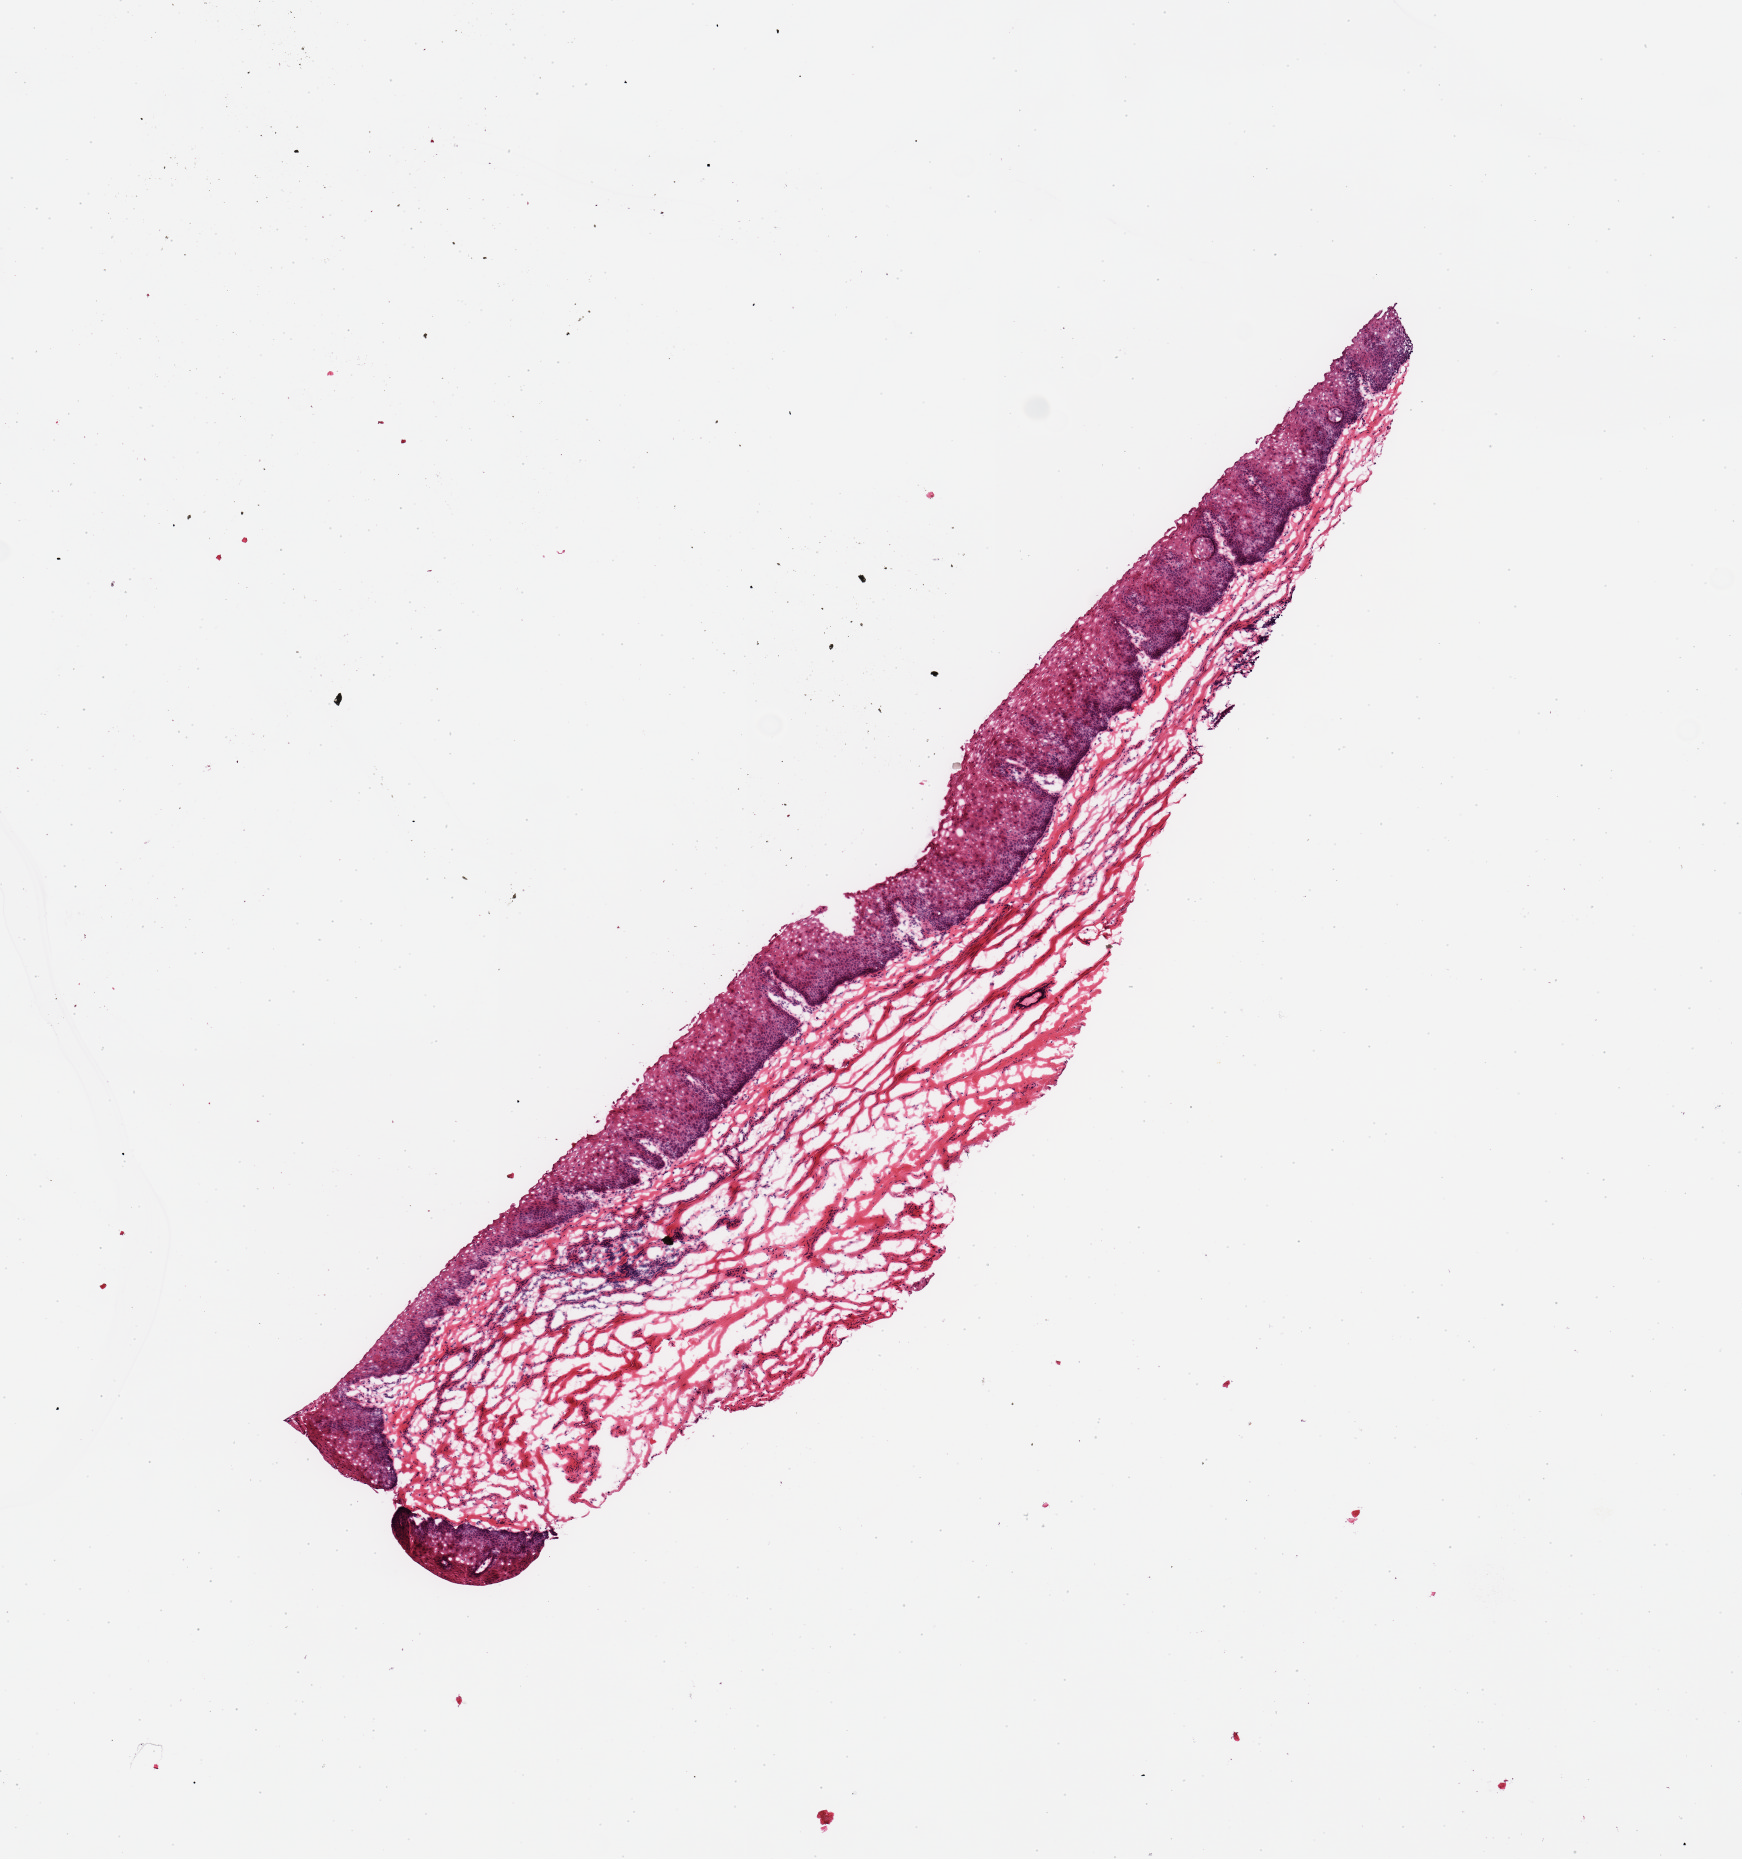
Digitized H&E-stained section, shown as a low-resolution overview of the whole scanned area (about 6.9 x 7.4 mm, from a 20x scan). Frozen section (dry ice). Target tissue: esophageal mucous membrane. Donor tissue sample.
• reviewer comment on this tissue sample: 1 piece